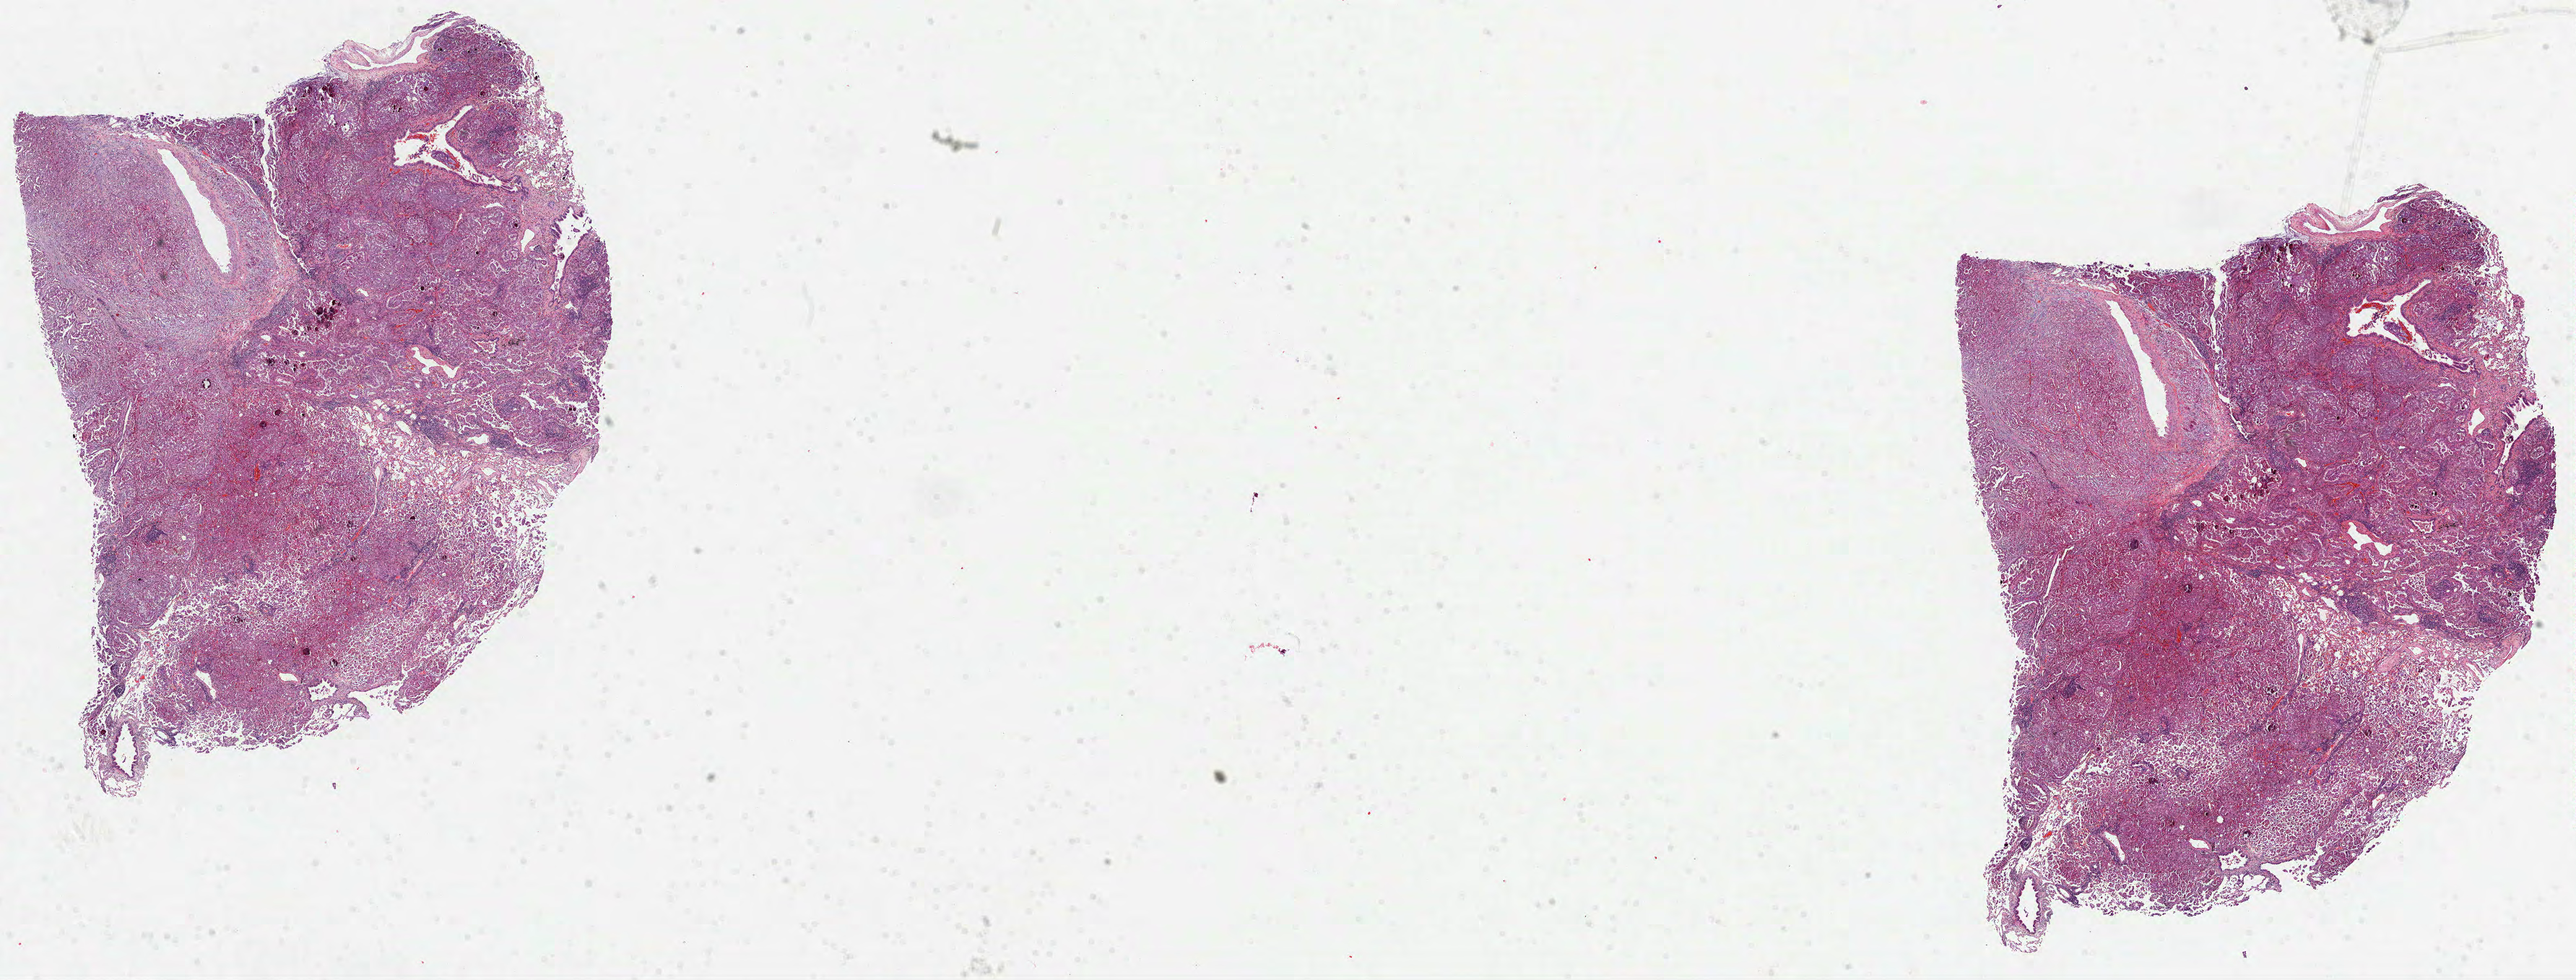
Whole-slide histology image, H&E — a low-resolution overview of the entire scanned area, about 28.8 x 10.9 mm (from a 40x scan). Formalin-fixed paraffin-embedded (FFPE) diagnostic section. Lung, primary tumour sample. Female, age 57 years at initial diagnosis.
Pathologic diagnosis: Adenocarcinoma, NOS (middle lobe, lung). AJCC pathologic stage: IA (7th edition).